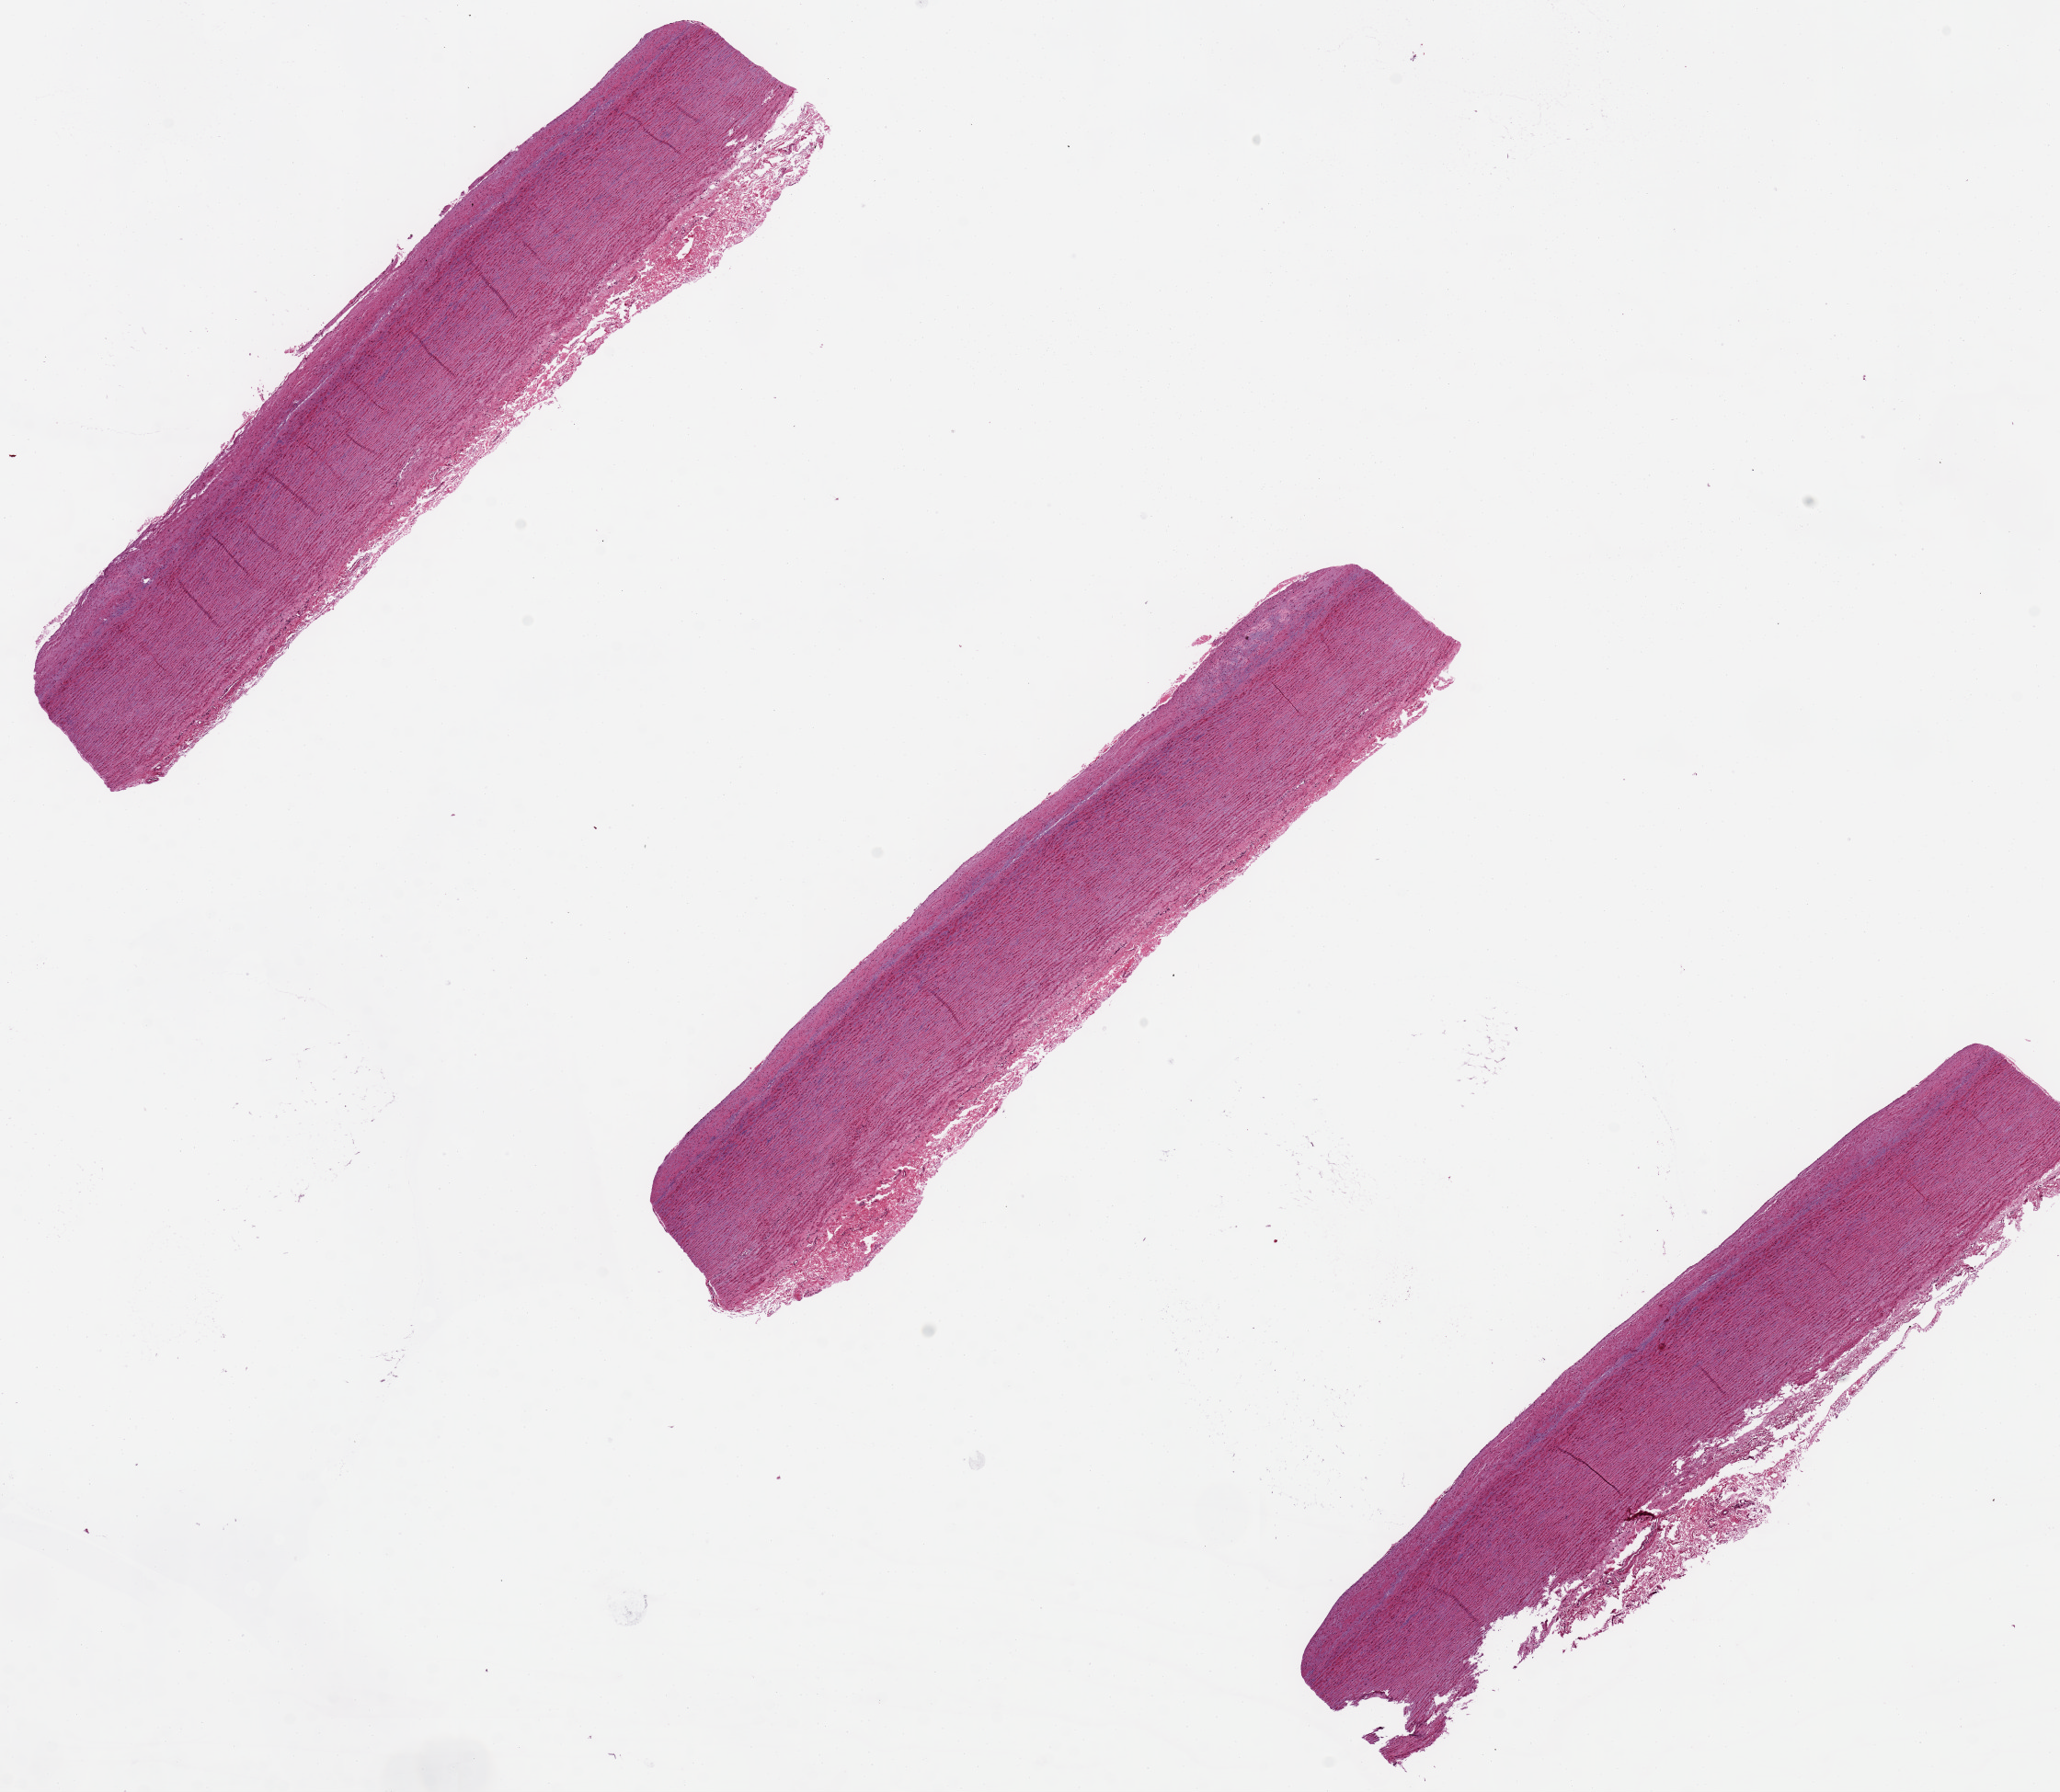
H&E whole-slide image — a low-resolution overview of the entire scanned area, about 17.7 x 15.4 mm (from a 20x scan), PAXgene-fixed paraffin-embedded (PFPE) section, sampled site (target tissue): aorta, tissue donor sample. Male donor.
Review note (as recorded): OK for analysis.